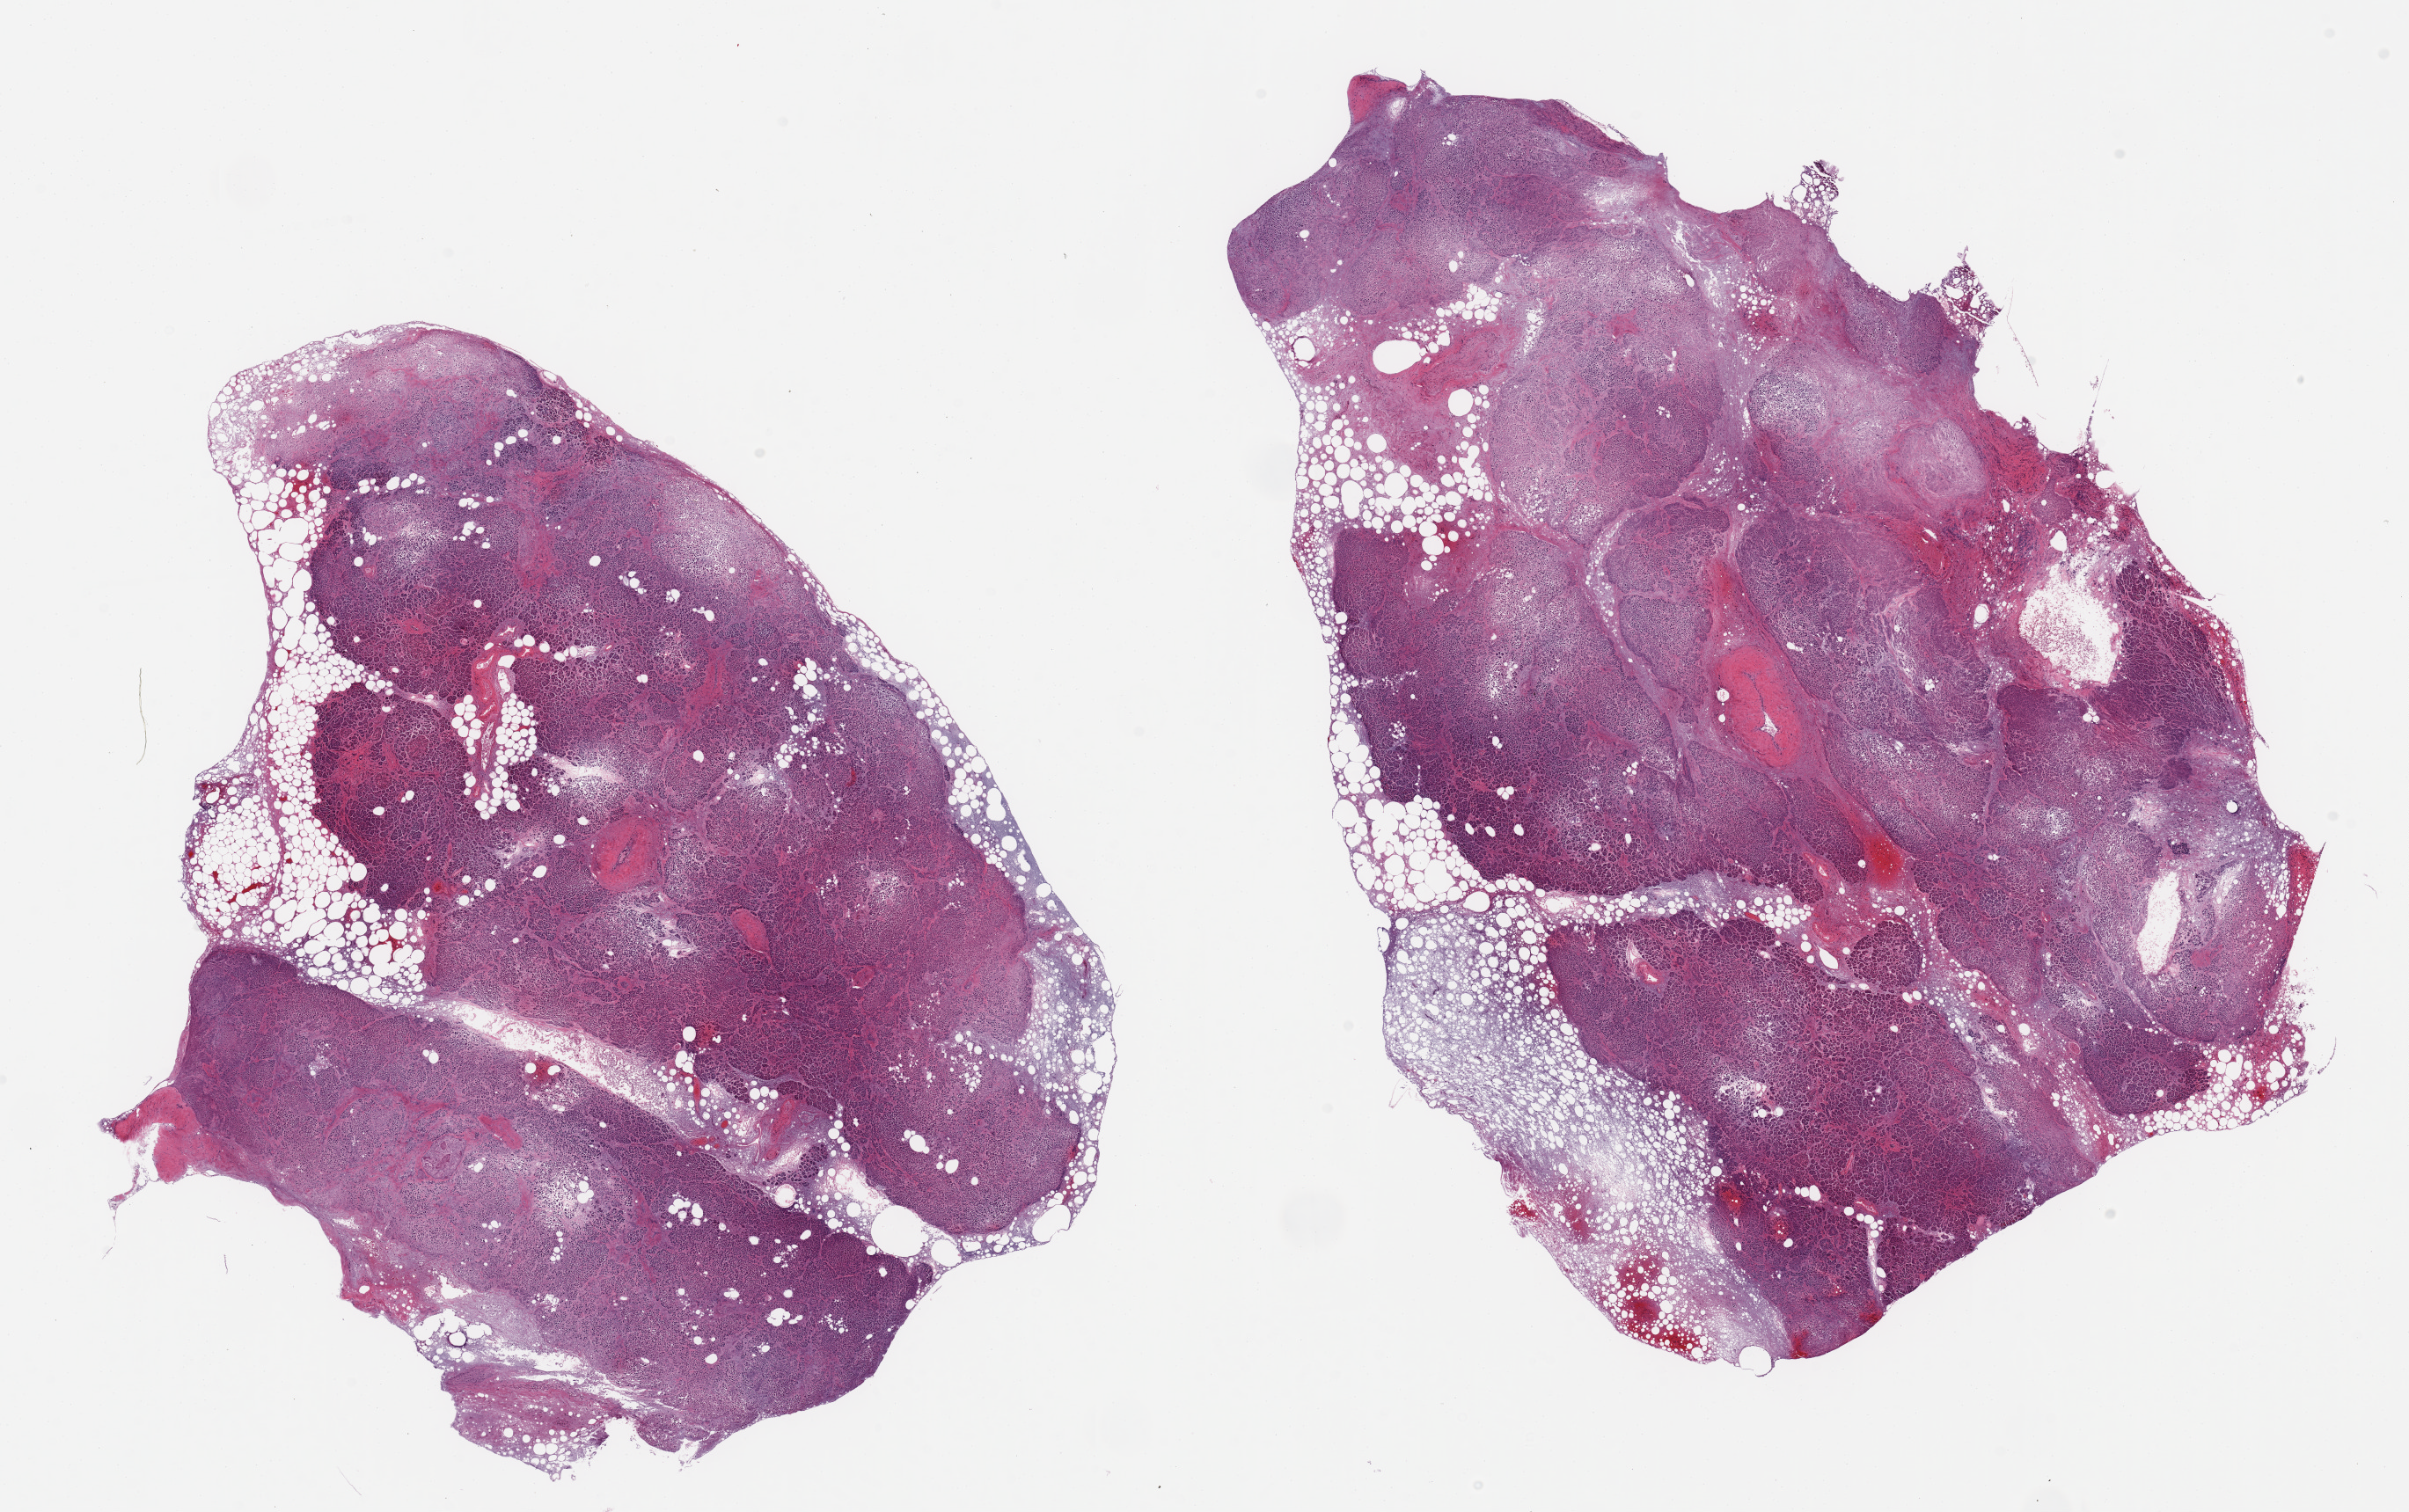
Whole-slide image, hematoxylin and eosin (H&E) stain, a low-resolution overview of the entire scanned area, about 21.7 x 13.6 mm; PAXgene-fixed paraffin-embedded (PFPE) section; section of pancreas (target tissue); donor tissue sample. Donor: male.
Review note (as recorded): 2 pieces; ~15% internal and ~20% external fat; severe autolysis; some residual islets.